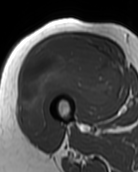
MRI of an extremity soft-tissue mass, one axial slice. Position 44 of 99 along the scan axis. MR volume resampled by the dataset authors to the PET/CT grid (not the native acquisition matrix). 3.27 mm slice thickness. 138 × 172 image matrix, field of view 135 × 168 mm. Female patient. Case-level facts recorded for this patient, not image findings: histological type: pleiomorphic undifferentiated sarcoma; grade: high; site of the primary tumour: right quadricep.
Structures marked on this image (expert contour drawn on MRI and transferred to this co-registered scan by the dataset authors):
- gross tumour volume including surrounding oedema: bounding box (x1, y1, x2, y2) in pixels: (21, 36, 120, 133)
- gross tumour volume (mass): (21, 36, 120, 133)